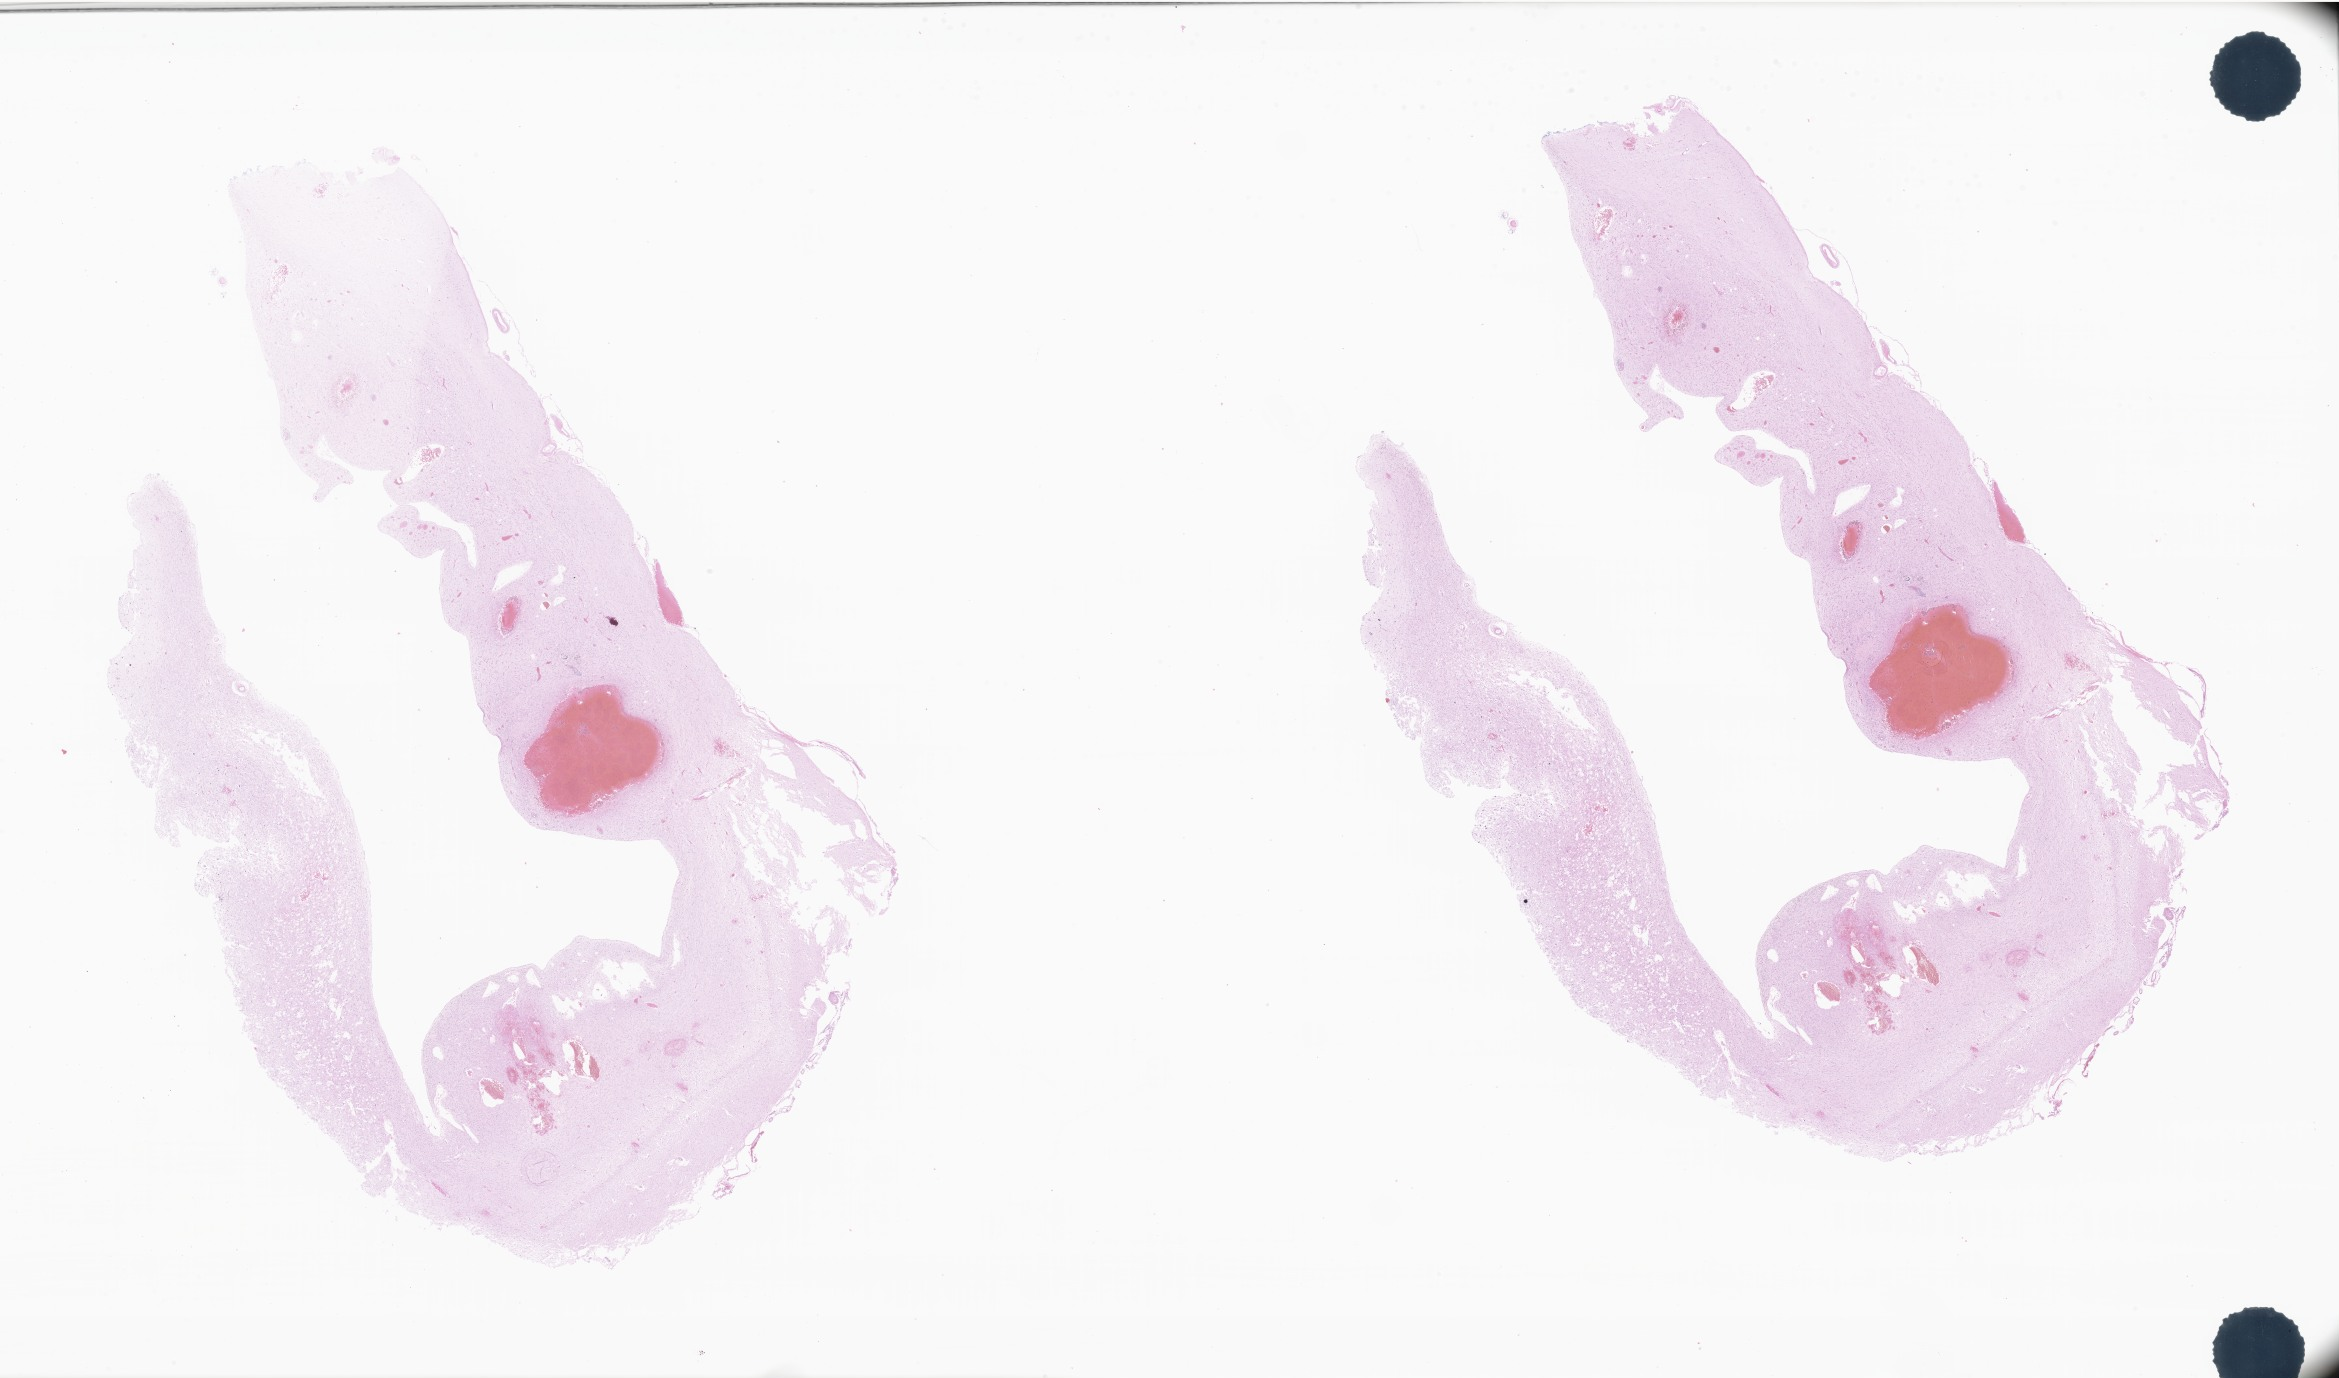
Whole-slide image, haematoxylin and eosin stain of tumor tissue from the temporal lobe — shown as a low-resolution overview of the whole scanned area (about 39.4 x 23.2 mm), FFPE section. Patient female; age 140 months (11 years 8 months).
Diagnosis (ICD-O-3 morphology term): Neuroepithelioma, NOS.